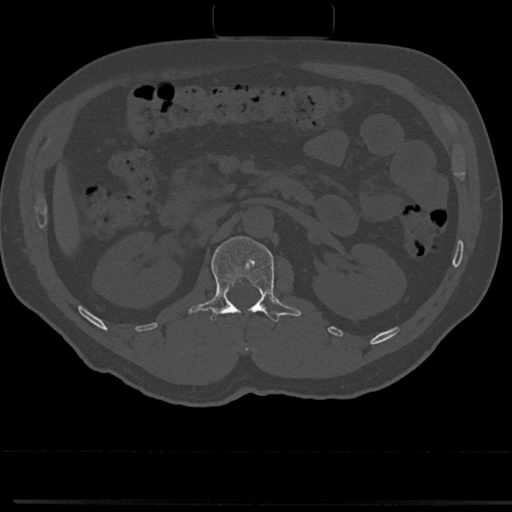
CT including the spine, one axial slice; position 82 of 817 along the scan axis; 120 kVp; bone window (W 1800 / L 400 HU); 0.5 mm slice thickness; 512 × 512 image matrix. Male patient, age 61 years. Case-level facts recorded for this patient, not image findings: primary cancer: prostate.
Outlined on this slice (semi-automatic segmentation, software-assisted and operator-edited):
- L1 vertebra: box from (x=190, y=237) to (x=300, y=323) px